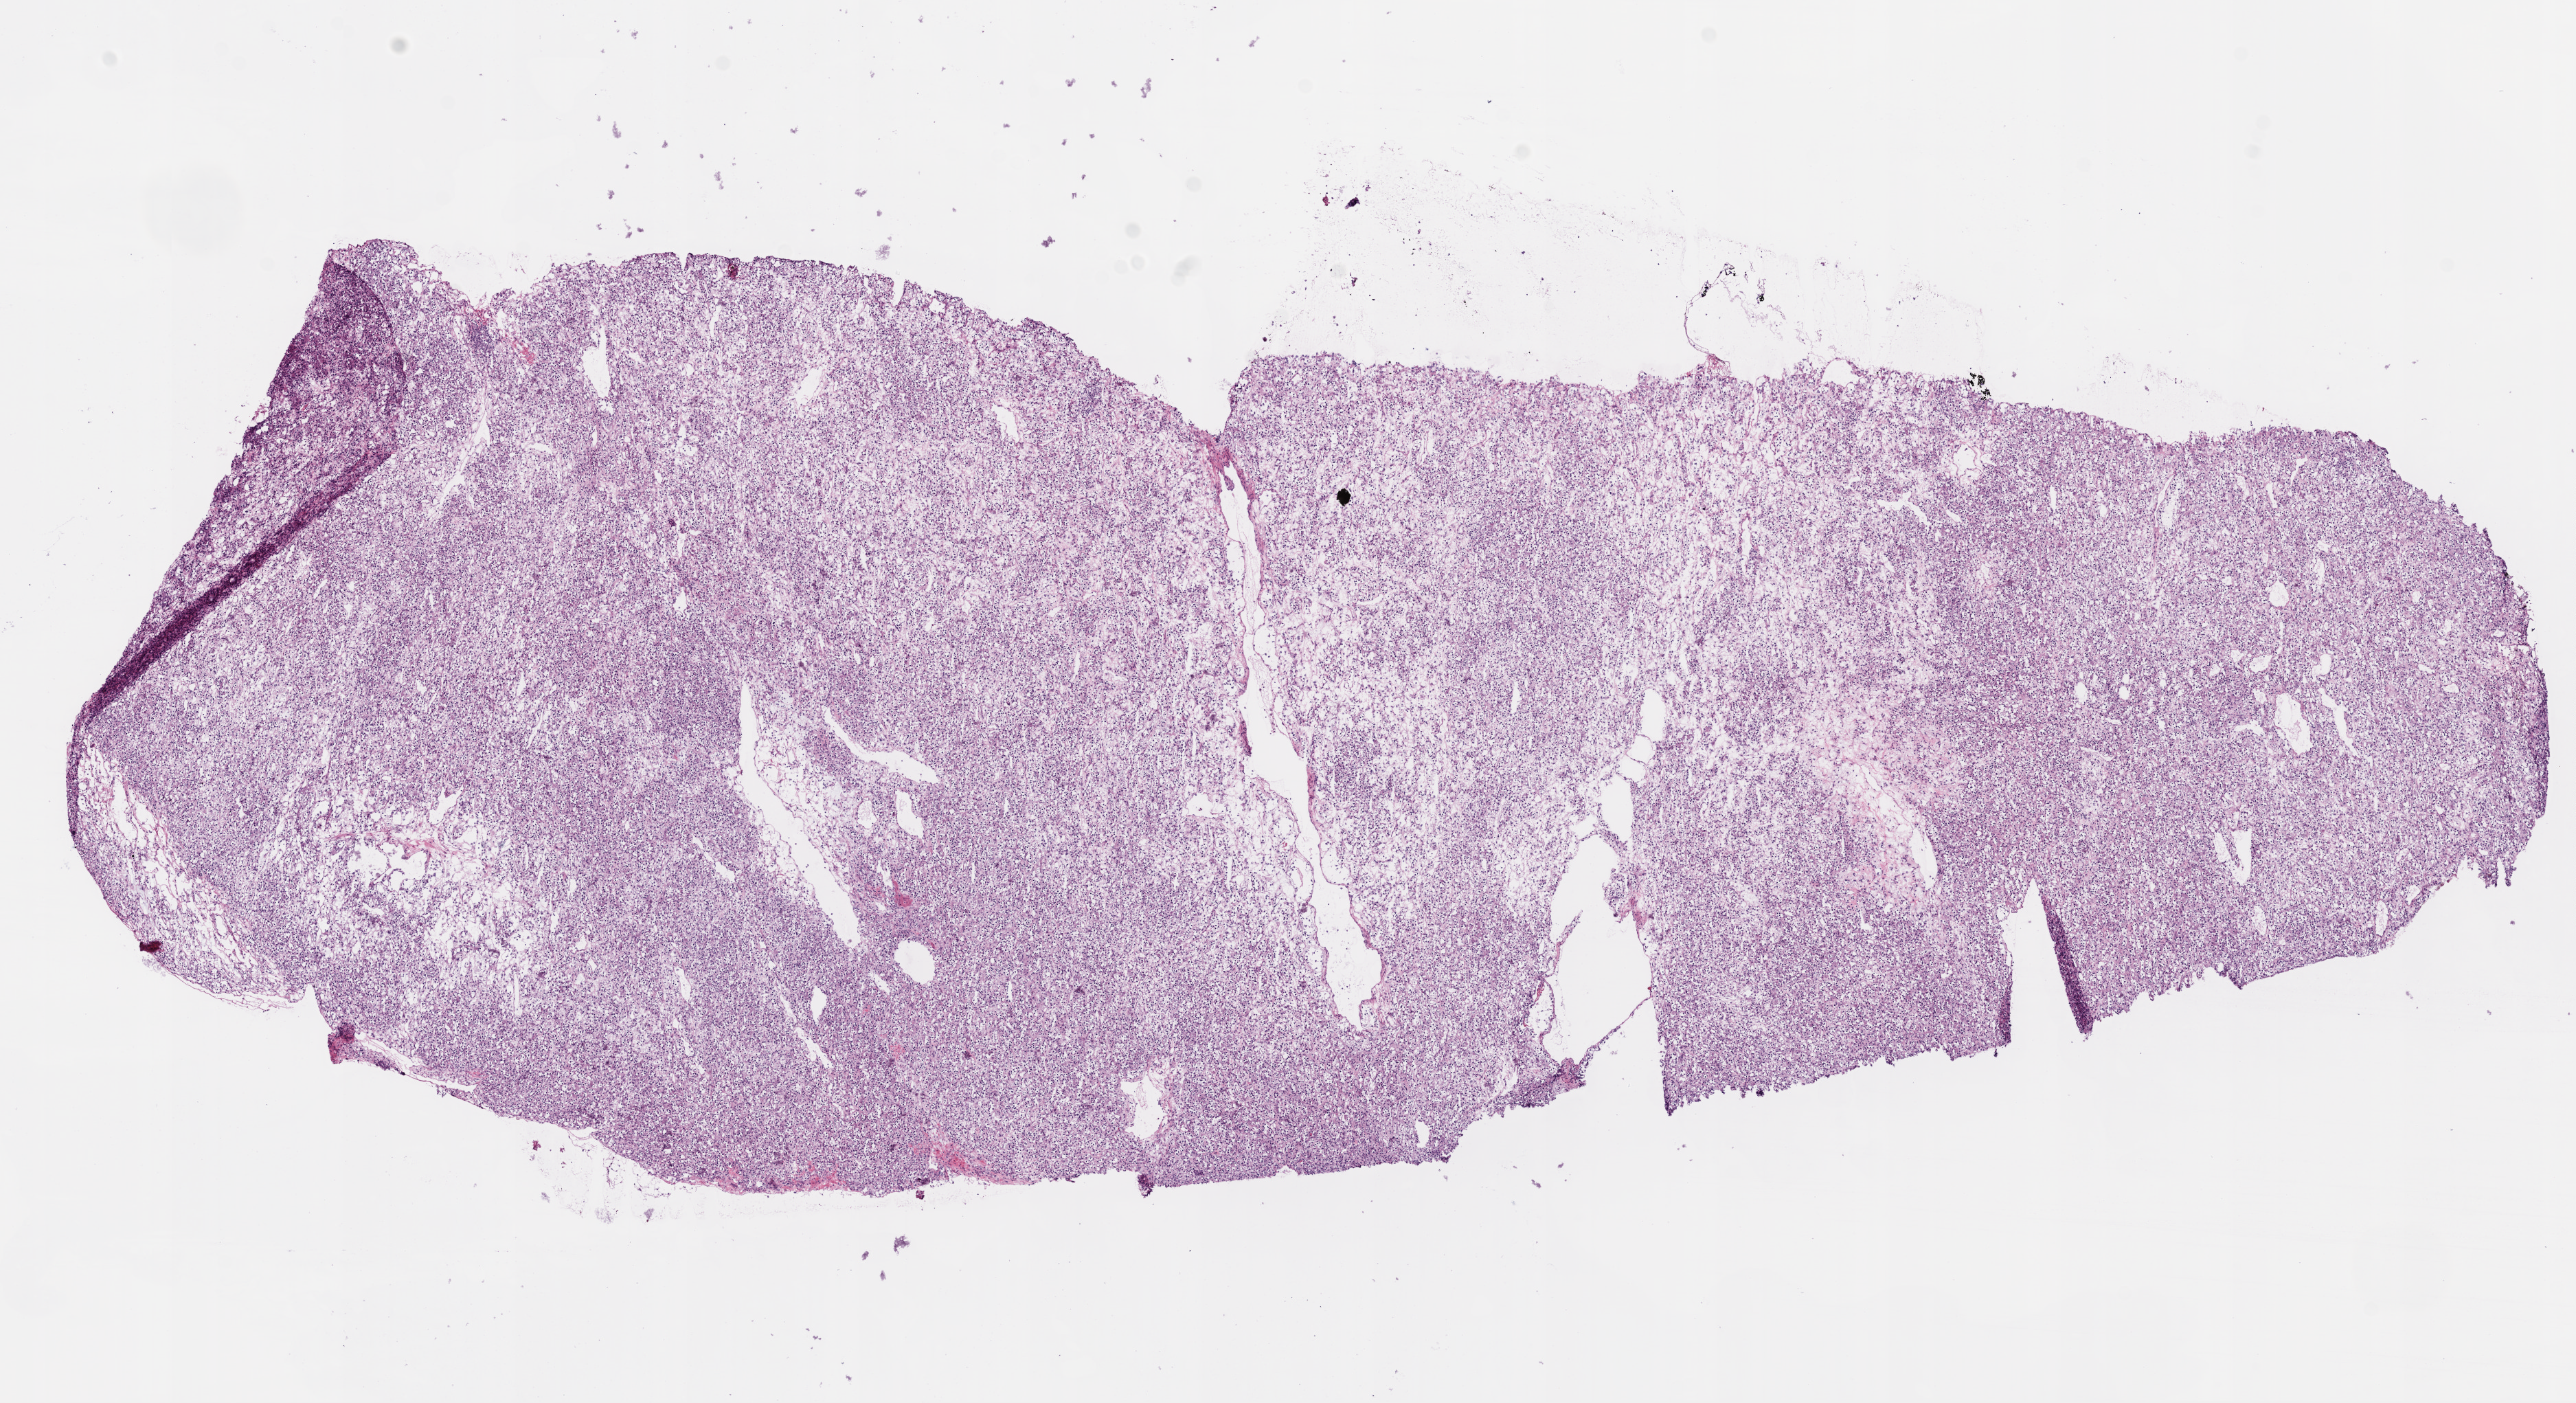
Whole-slide histology image, H&E — a low-resolution overview of the entire scanned area, about 15.0 x 8.2 mm. Frozen section. Sample: primary tumour, kidney. Patient: male, age at initial diagnosis 52 years. Histologic grade: G2 (moderately differentiated). Pathologist review of this section (percent, as recorded): tumour cells 95%, tumour nuclei 80%, normal cells 0%, stromal cells 5%, necrosis 0%.
- AJCC pathologic stage: I
- pathologic diagnosis: Clear cell adenocarcinoma, NOS